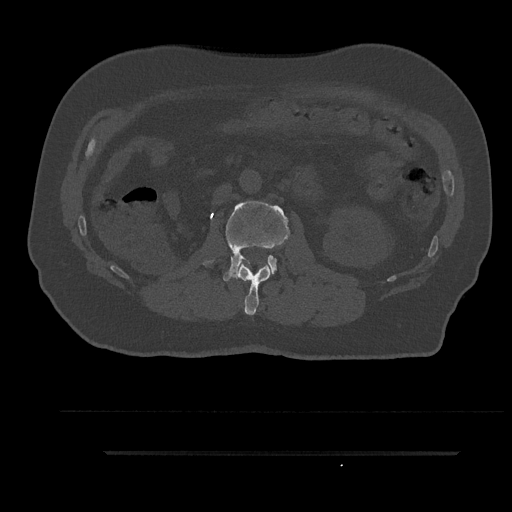
CT including the spine, one axial slice. Slice 135 of 797 in the series (ordered by position). 120 kVp. Bone window (W 1800 / L 400 HU). 0.5 mm slice thickness. 512 × 512 image matrix, field of view 432 × 432 mm. Male patient, age 63 years. From the clinical record (not read from this slice): primary cancer: renal.
Annotated regions visible in this slice (semi-automatically segmented with operator editing):
- L1 vertebra: bounding box <232,264,271,315> (left, top, right, bottom; pixels)
- L2 vertebra: <204,201,291,281>